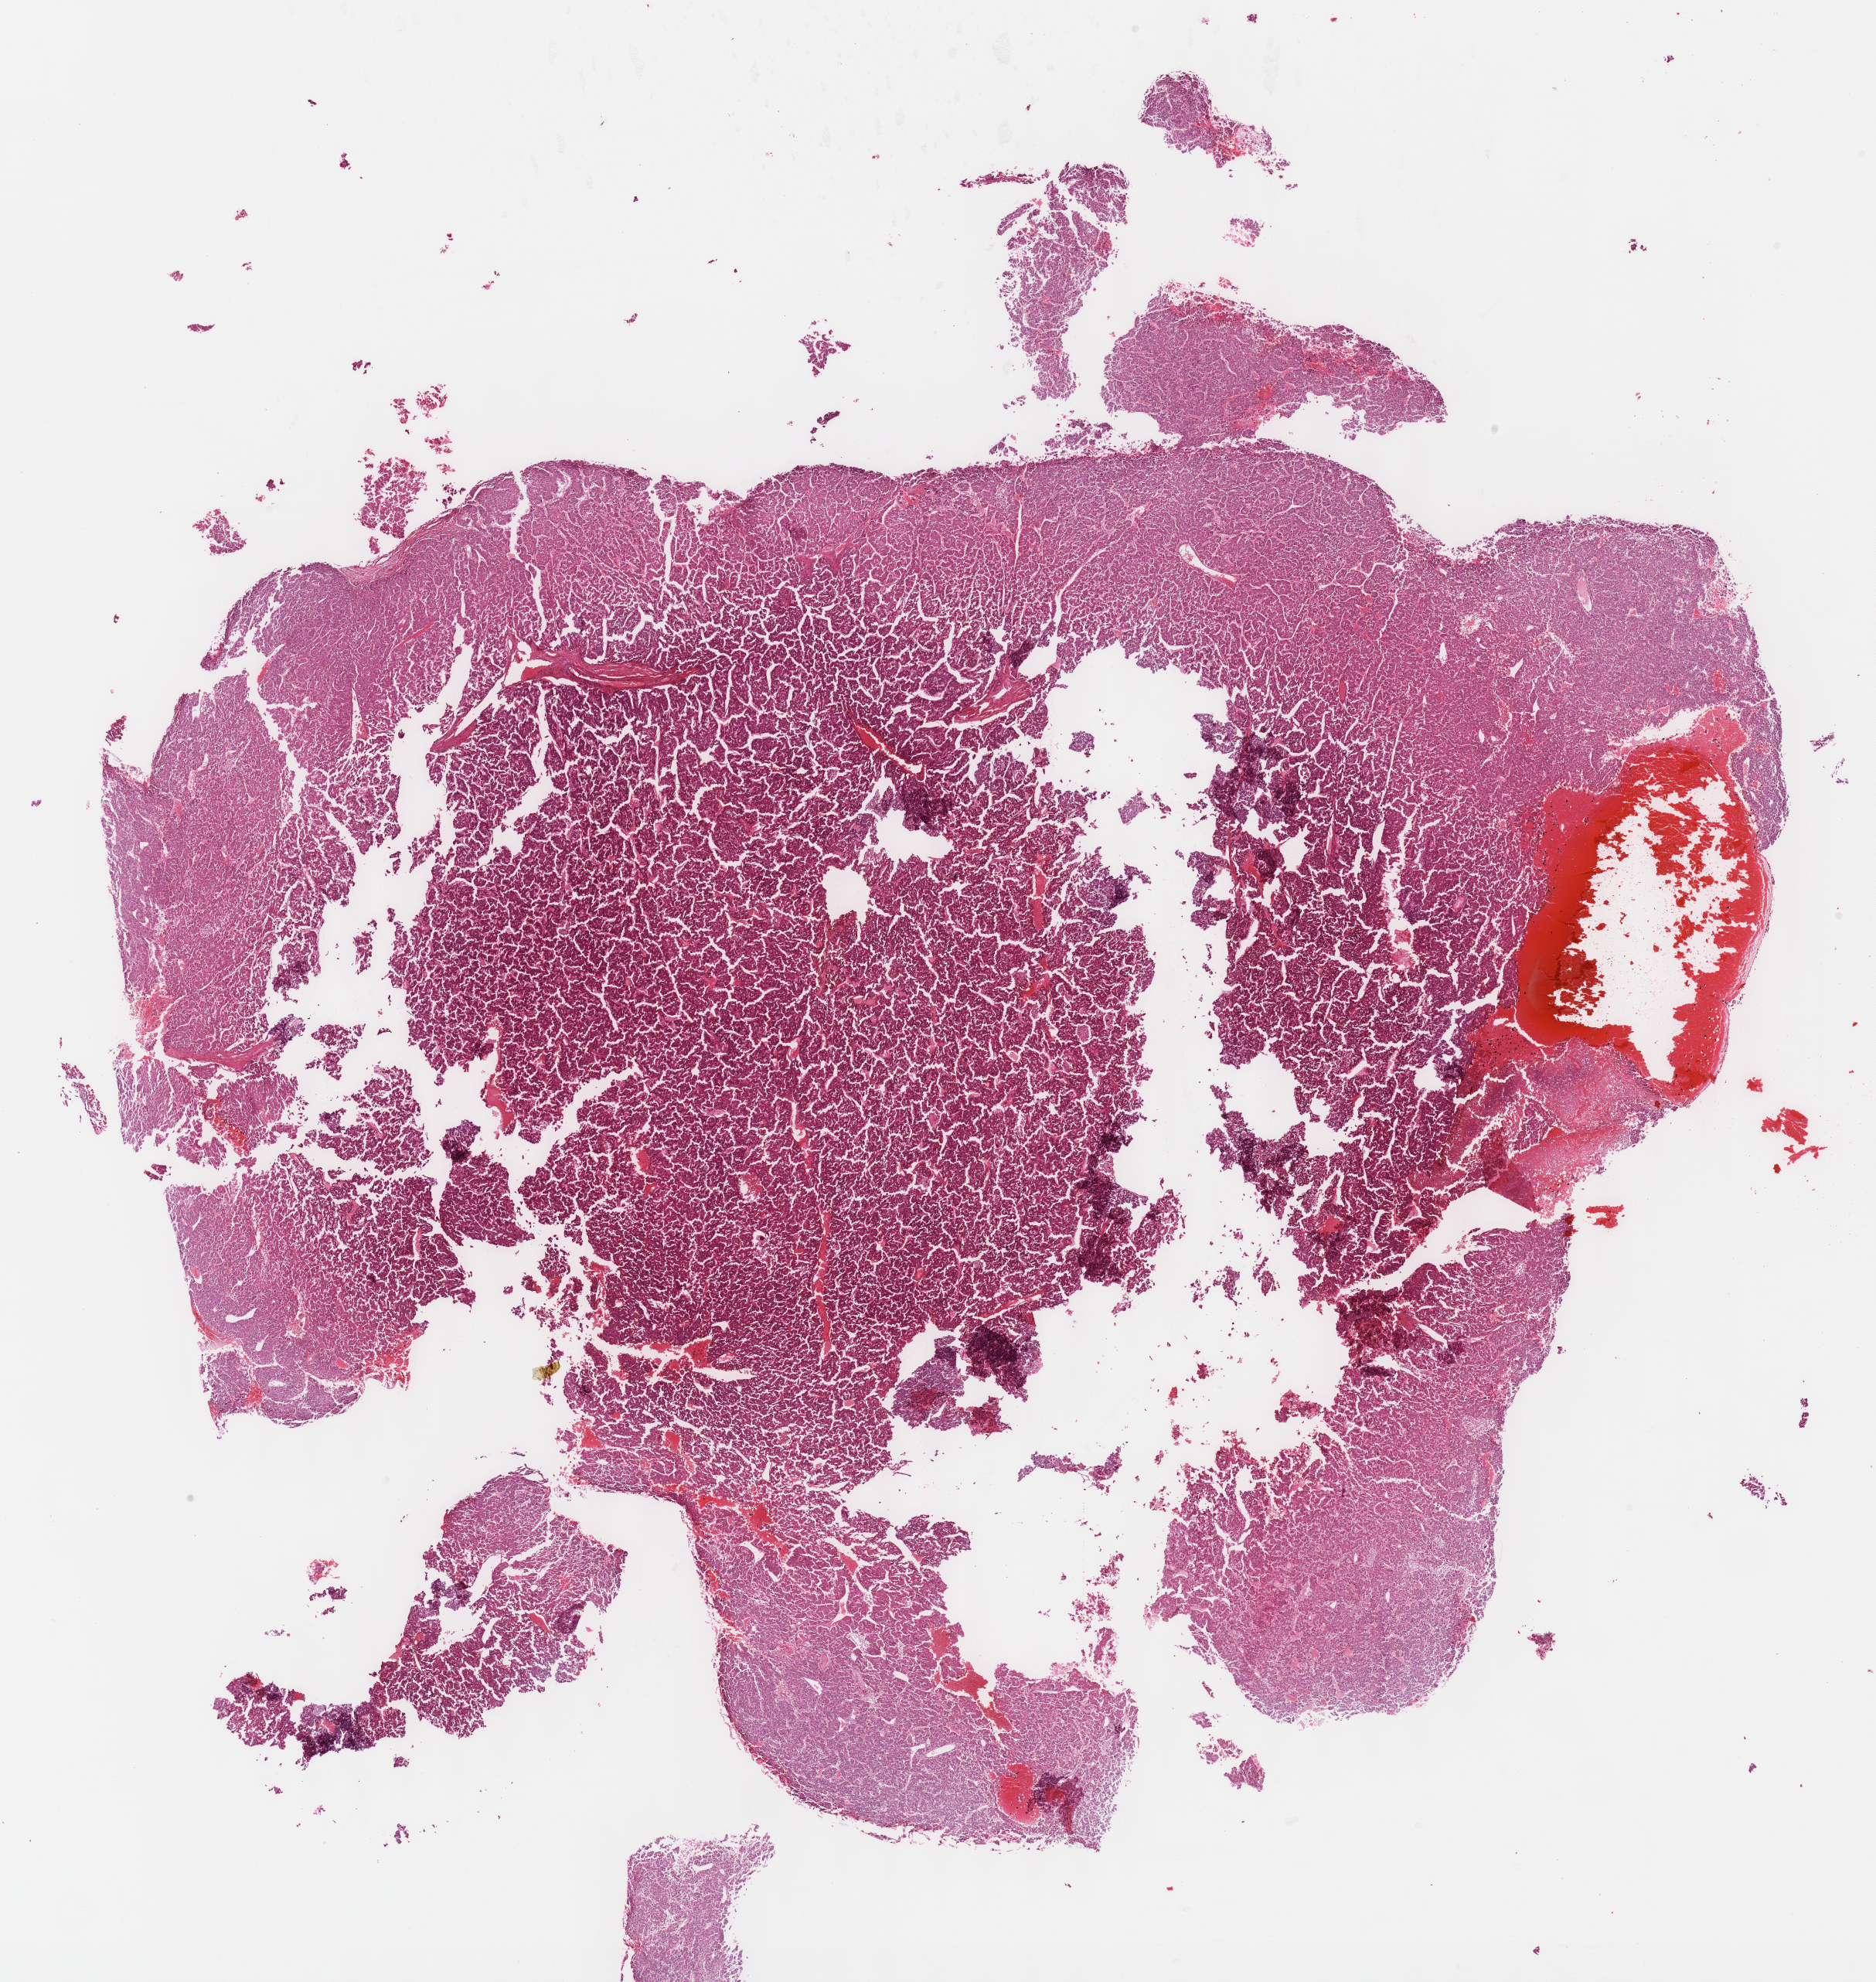
Whole-slide histology image, Hematoxylin and eosin (H&E) stained, shown as a low-resolution overview of the whole scanned area (about 19.6 x 20.7 mm). Formalin-fixed paraffin-embedded (FFPE) diagnostic section. Sample: primary tumour, liver. Patient: male, age at initial diagnosis 54 years. Histologic grade: G3 (poorly differentiated).
* AJCC pathologic stage: I (7th edition)
* histologic diagnosis: Hepatocellular carcinoma, NOS